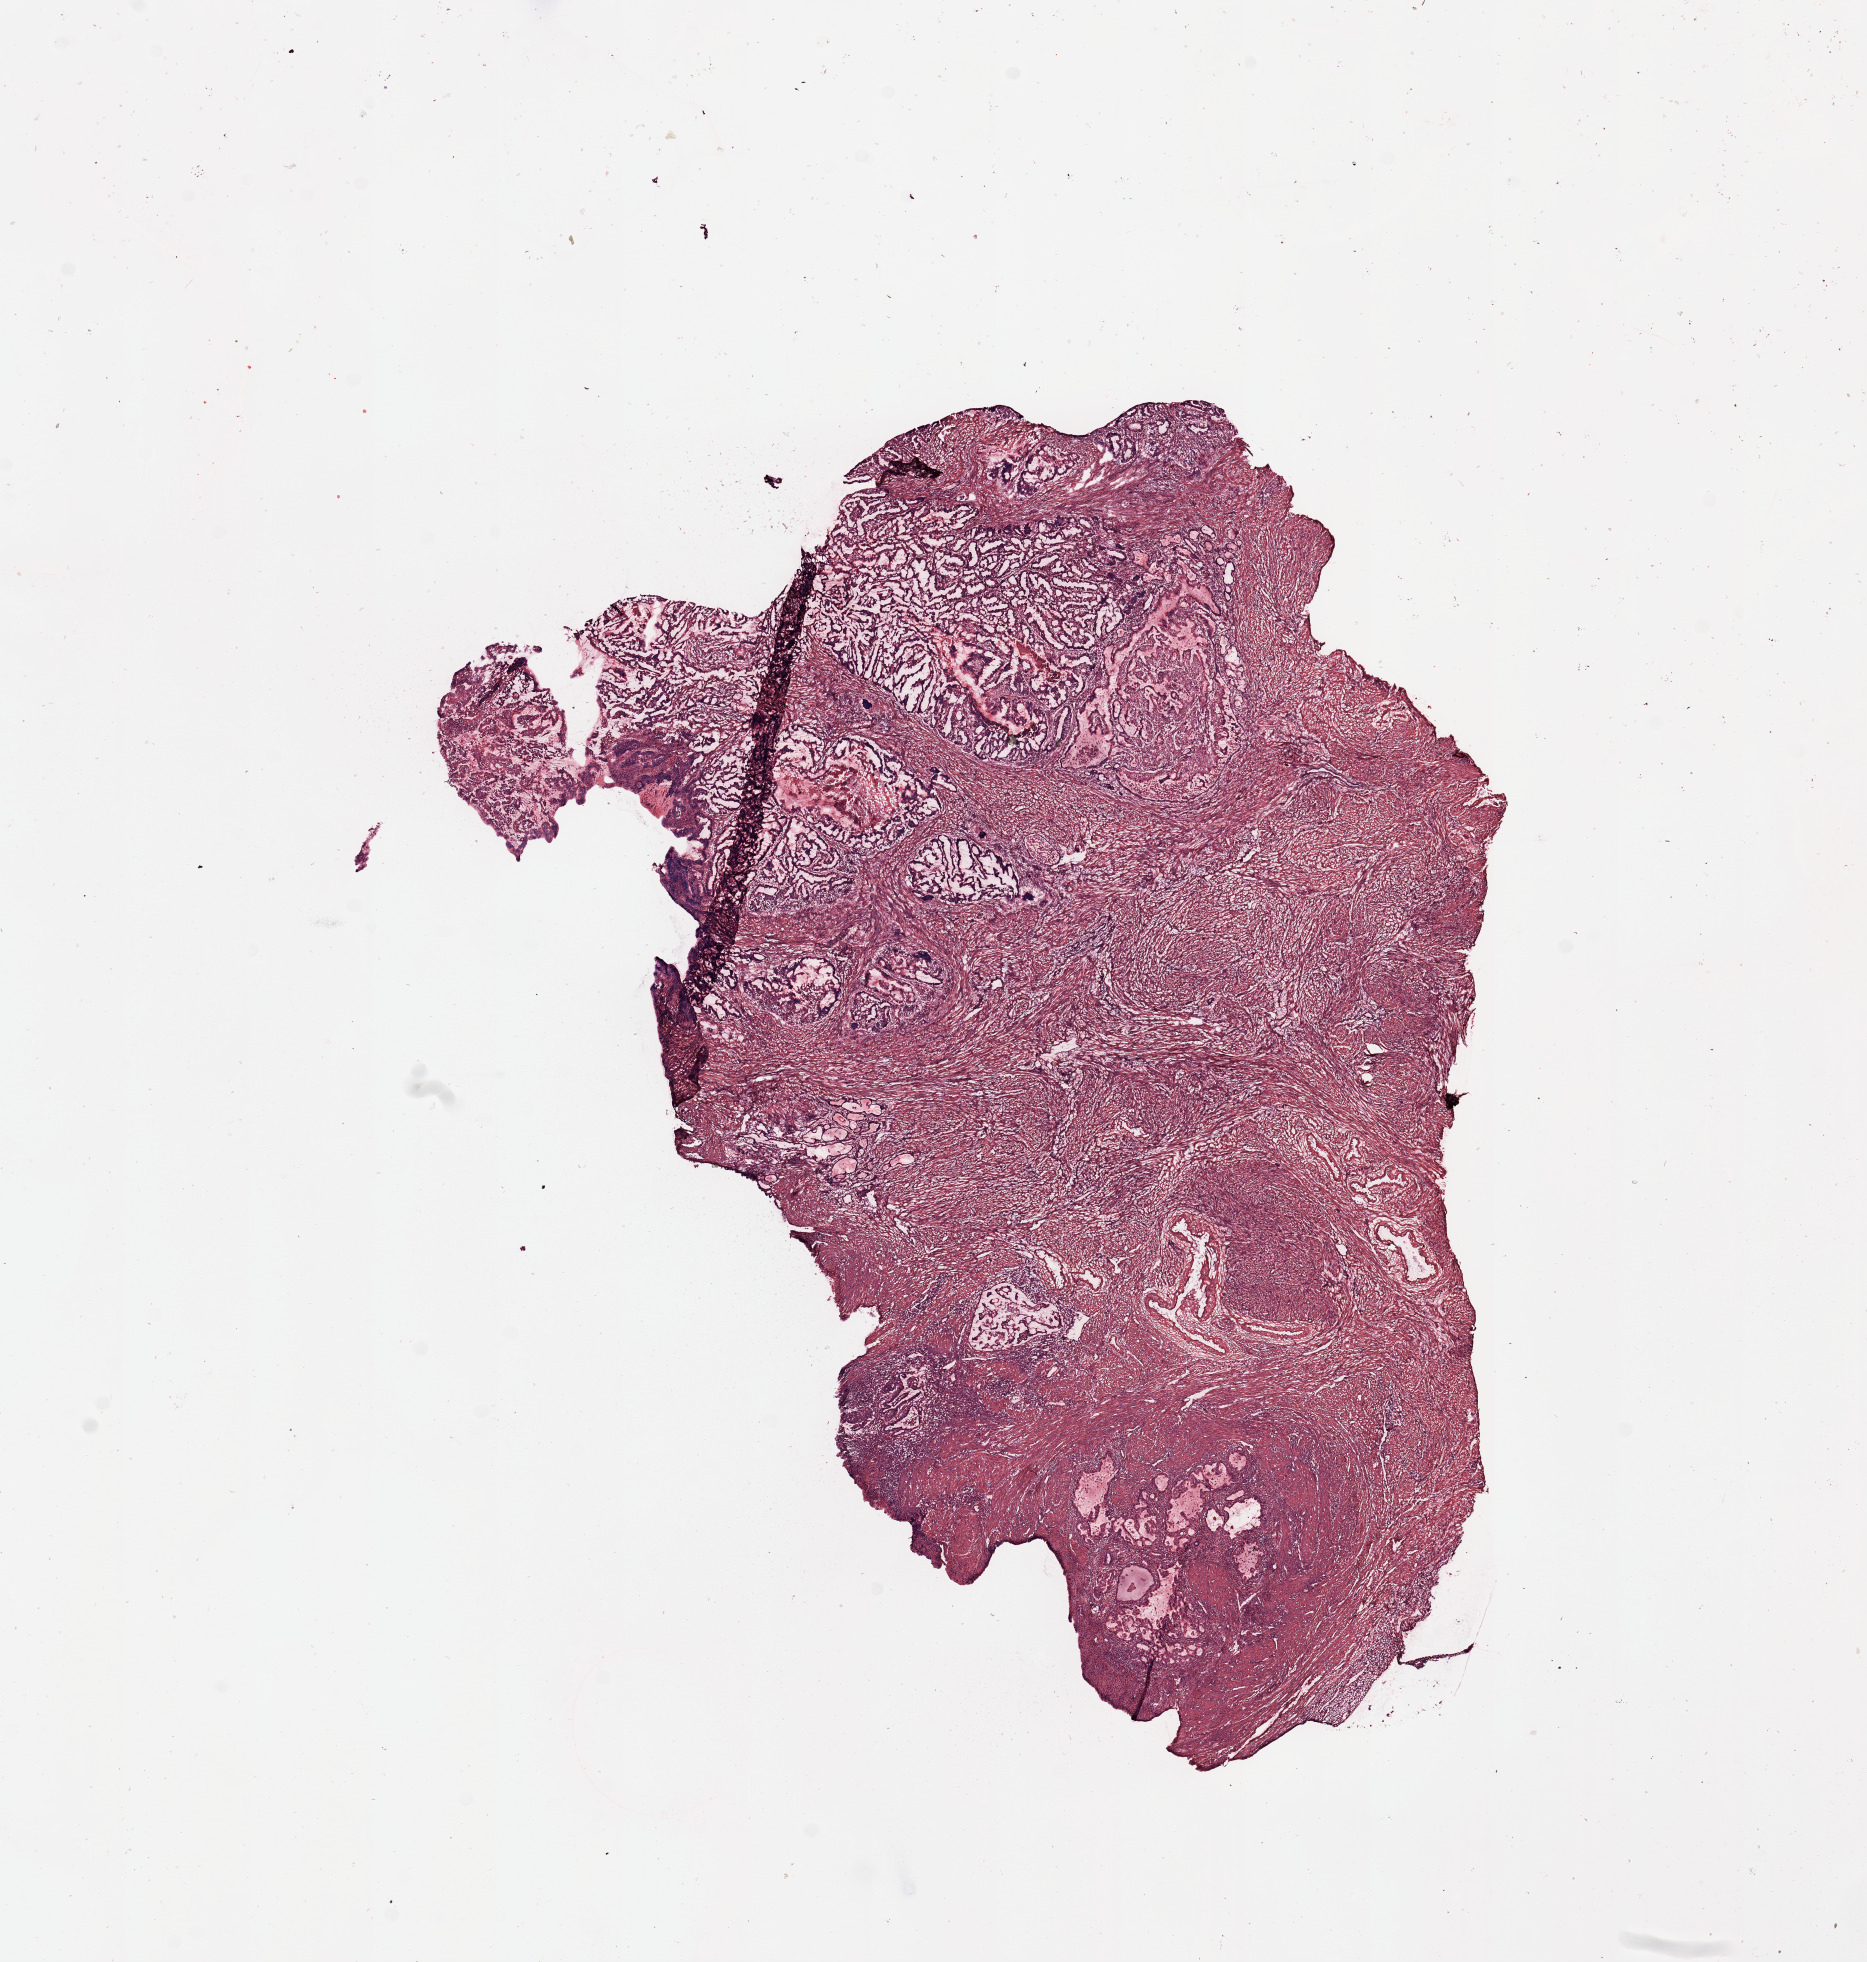
Digitized Hematoxylin and eosin (H&E) stained tissue section (whole slide) — low-resolution overview of the scanned area, about 14.8 x 15.5 mm (slide scanned at 20x), uterus, tumour tissue. 68-year-old female patient.
Diagnosis: Endometrioid adenocarcinoma, NOS.